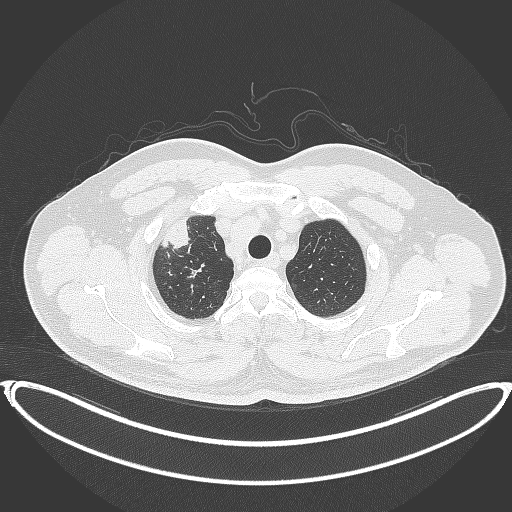
Chest CT, one axial slice; position 337 of 399 along the scan axis; 120 kVp; lung window (W 1500 / L -600 HU); 512 × 512 image matrix, field of view 445 × 445 mm. Patient: male, 53 years. Case-level facts recorded for this patient, not image findings: clinical TNM (as recorded): T2a N0 M0.
Structures marked on this image (bounding box drawn by a radiologist):
- lung tumour (recorded histology: adenocarcinoma): bounding box [x1, y1, x2, y2] px = [156, 213, 197, 254]